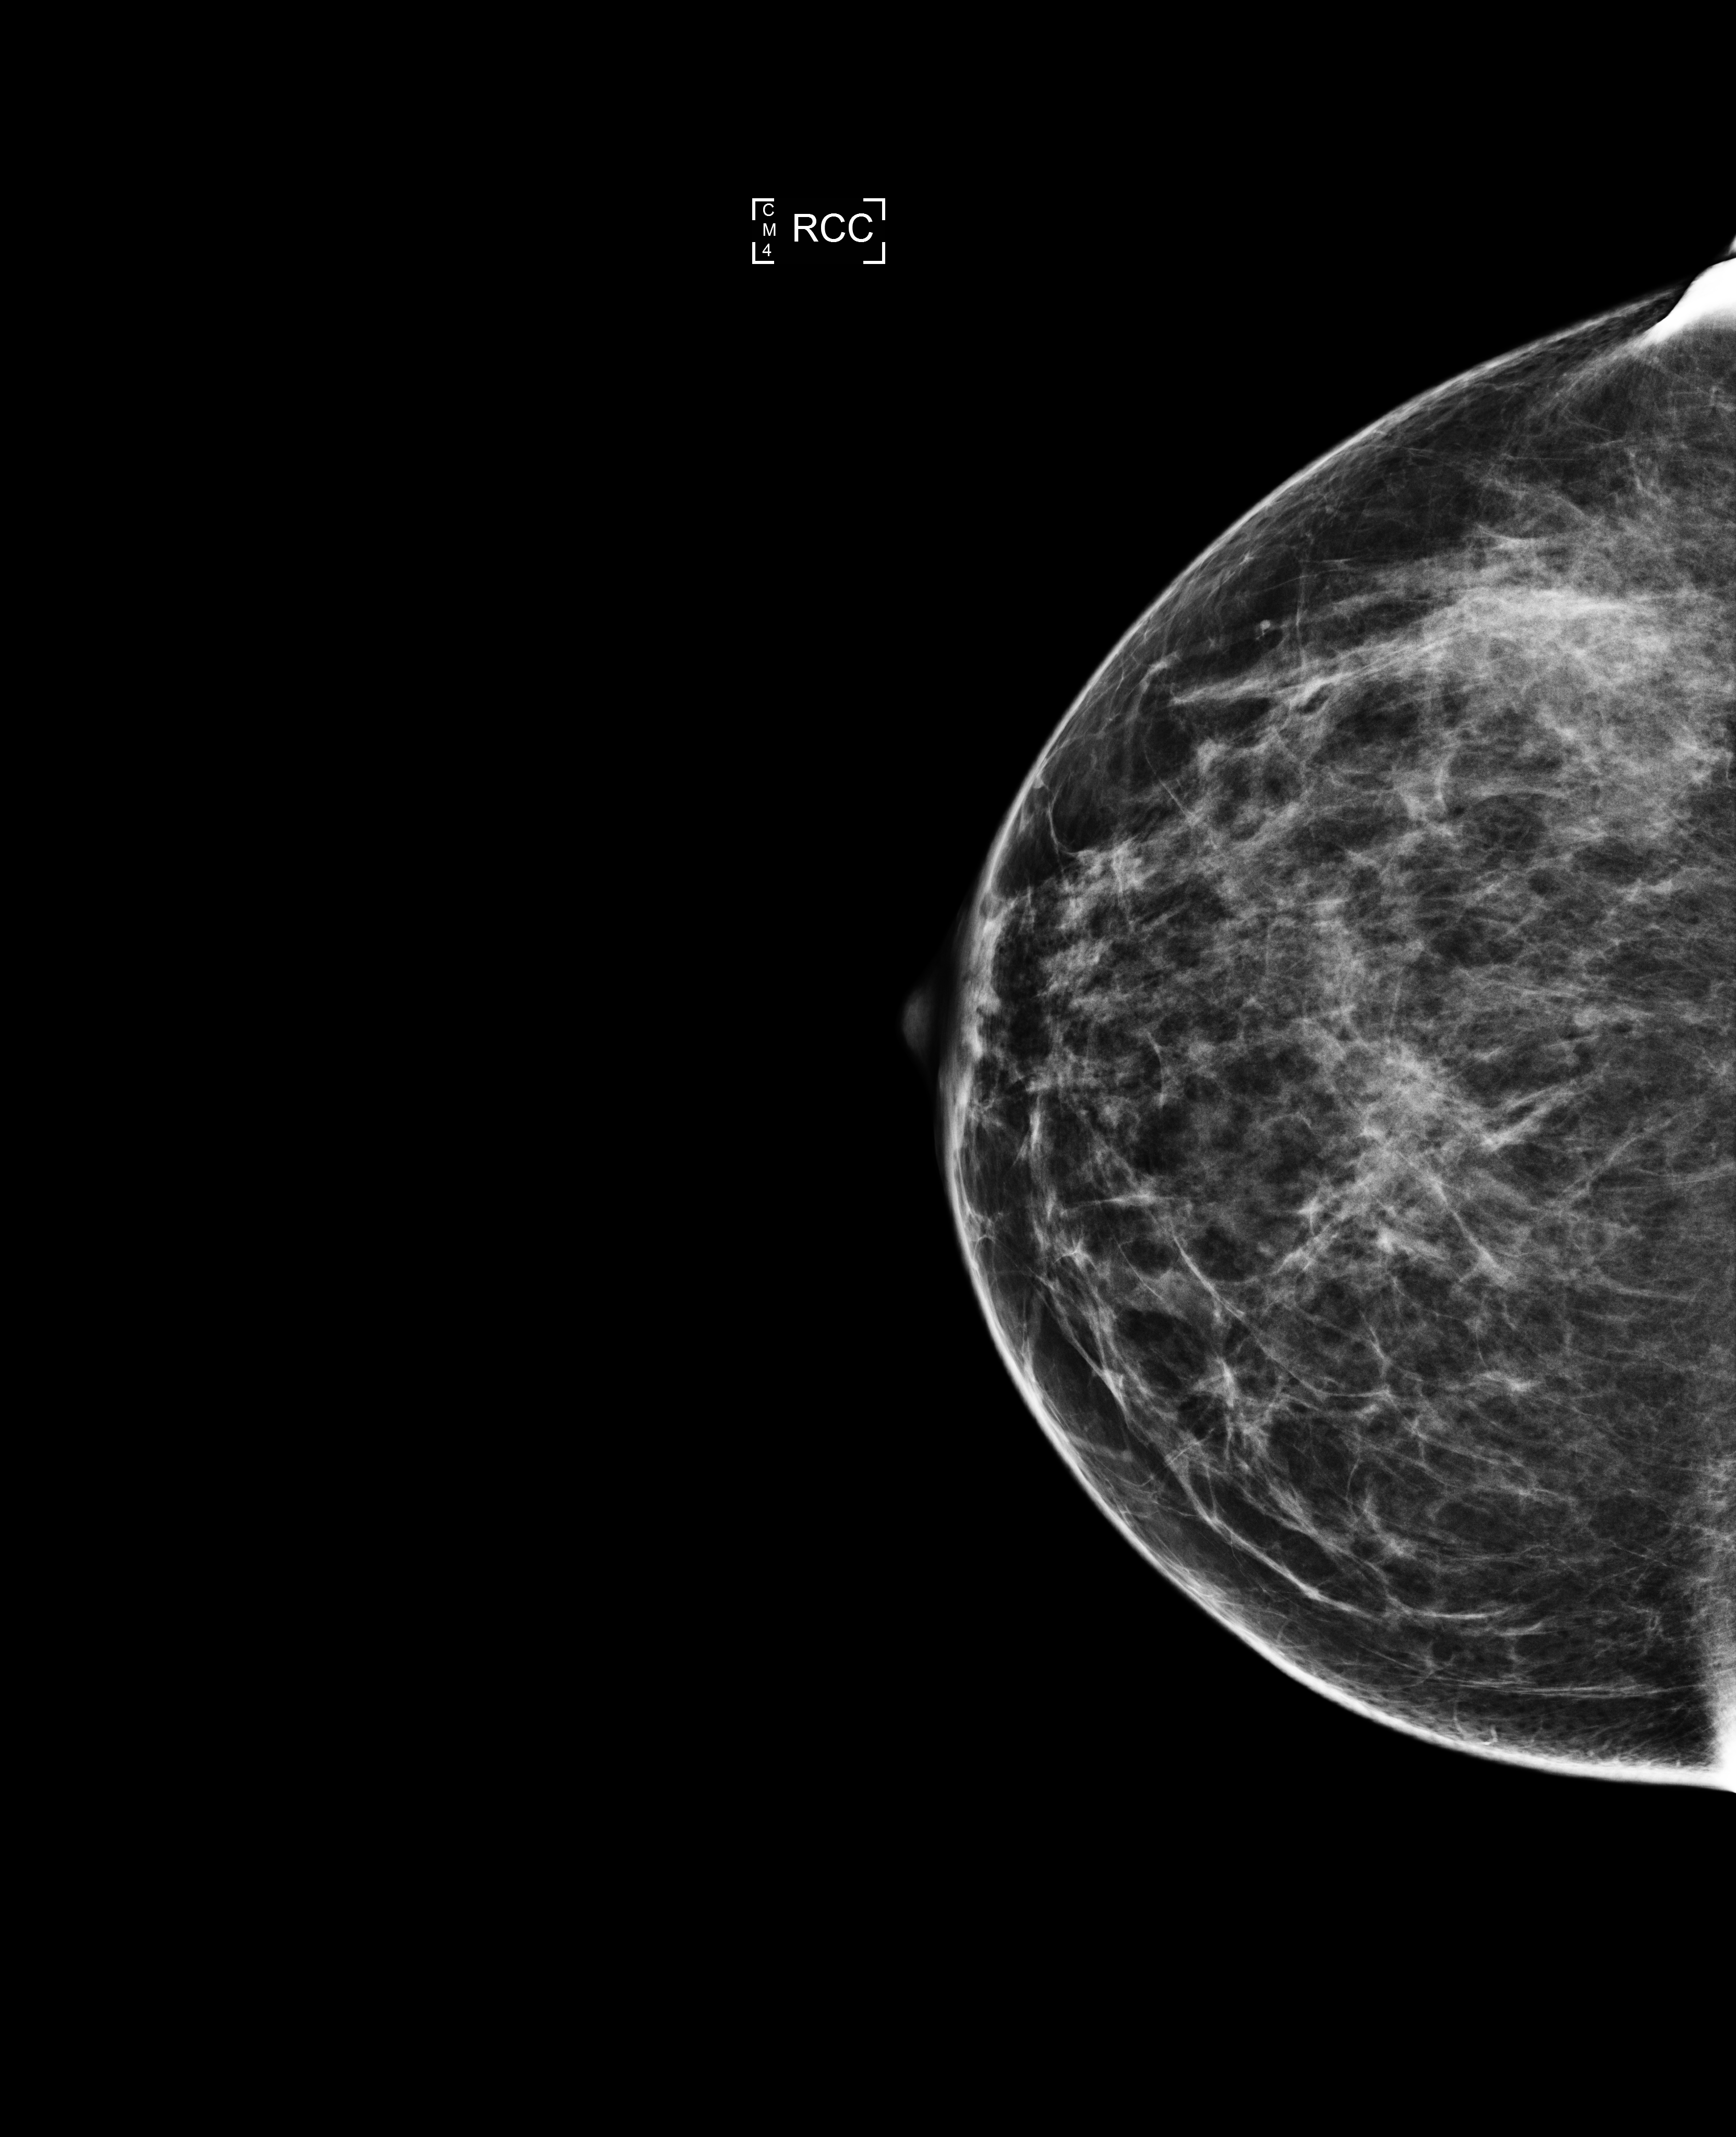
Annual screening mammography examination; system: Selenia Dimensions. Patient: female, 46 years.
Image type: full-field digital mammogram. Breast: right. Projection: cranio-caudal projection.